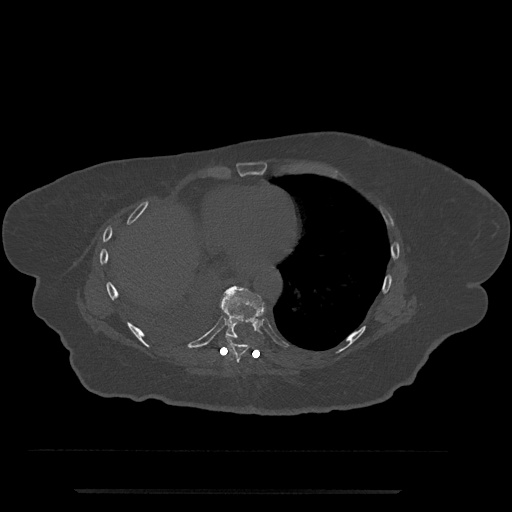
CT including the spine, one axial slice; position 367 of 797 along the scan axis; reconstruction kernel Br40s/3; 120 kVp; bone window (W 1800 / L 400 HU); 0.5 mm slice thickness; 512 × 512 image matrix, field of view 440 × 440 mm. Patient: female, 51 years. From the clinical record (not read from this slice): primary cancer: neuro; vertebrae with lytic lesions (as recorded): T8.
Annotated regions visible in this slice (semi-automatically segmented with operator editing):
- T8 vertebra: bounding box (x1, y1, x2, y2) in pixels: (225, 336, 249, 363)
- T9 vertebra: (218, 286, 266, 339)